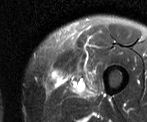
MRI of an extremity soft-tissue mass, one axial slice; position 8 of 52 along the scan axis; T2-weighted fat-saturated; MR volume resampled by the dataset authors to the PET/CT grid (not the native acquisition matrix); 147 × 122 image matrix, field of view 144 × 119 mm. Male patient. Case-level facts recorded for this patient, not image findings: histological type: pleiomorphic liposarcoma; grade: high; site of the primary tumour: left thigh.
Structures marked on this image (expert contour drawn on MRI and transferred to this co-registered scan by the dataset authors):
- gross tumour volume including surrounding oedema: bounding box (x1, y1, x2, y2) in pixels: (66, 66, 92, 95)